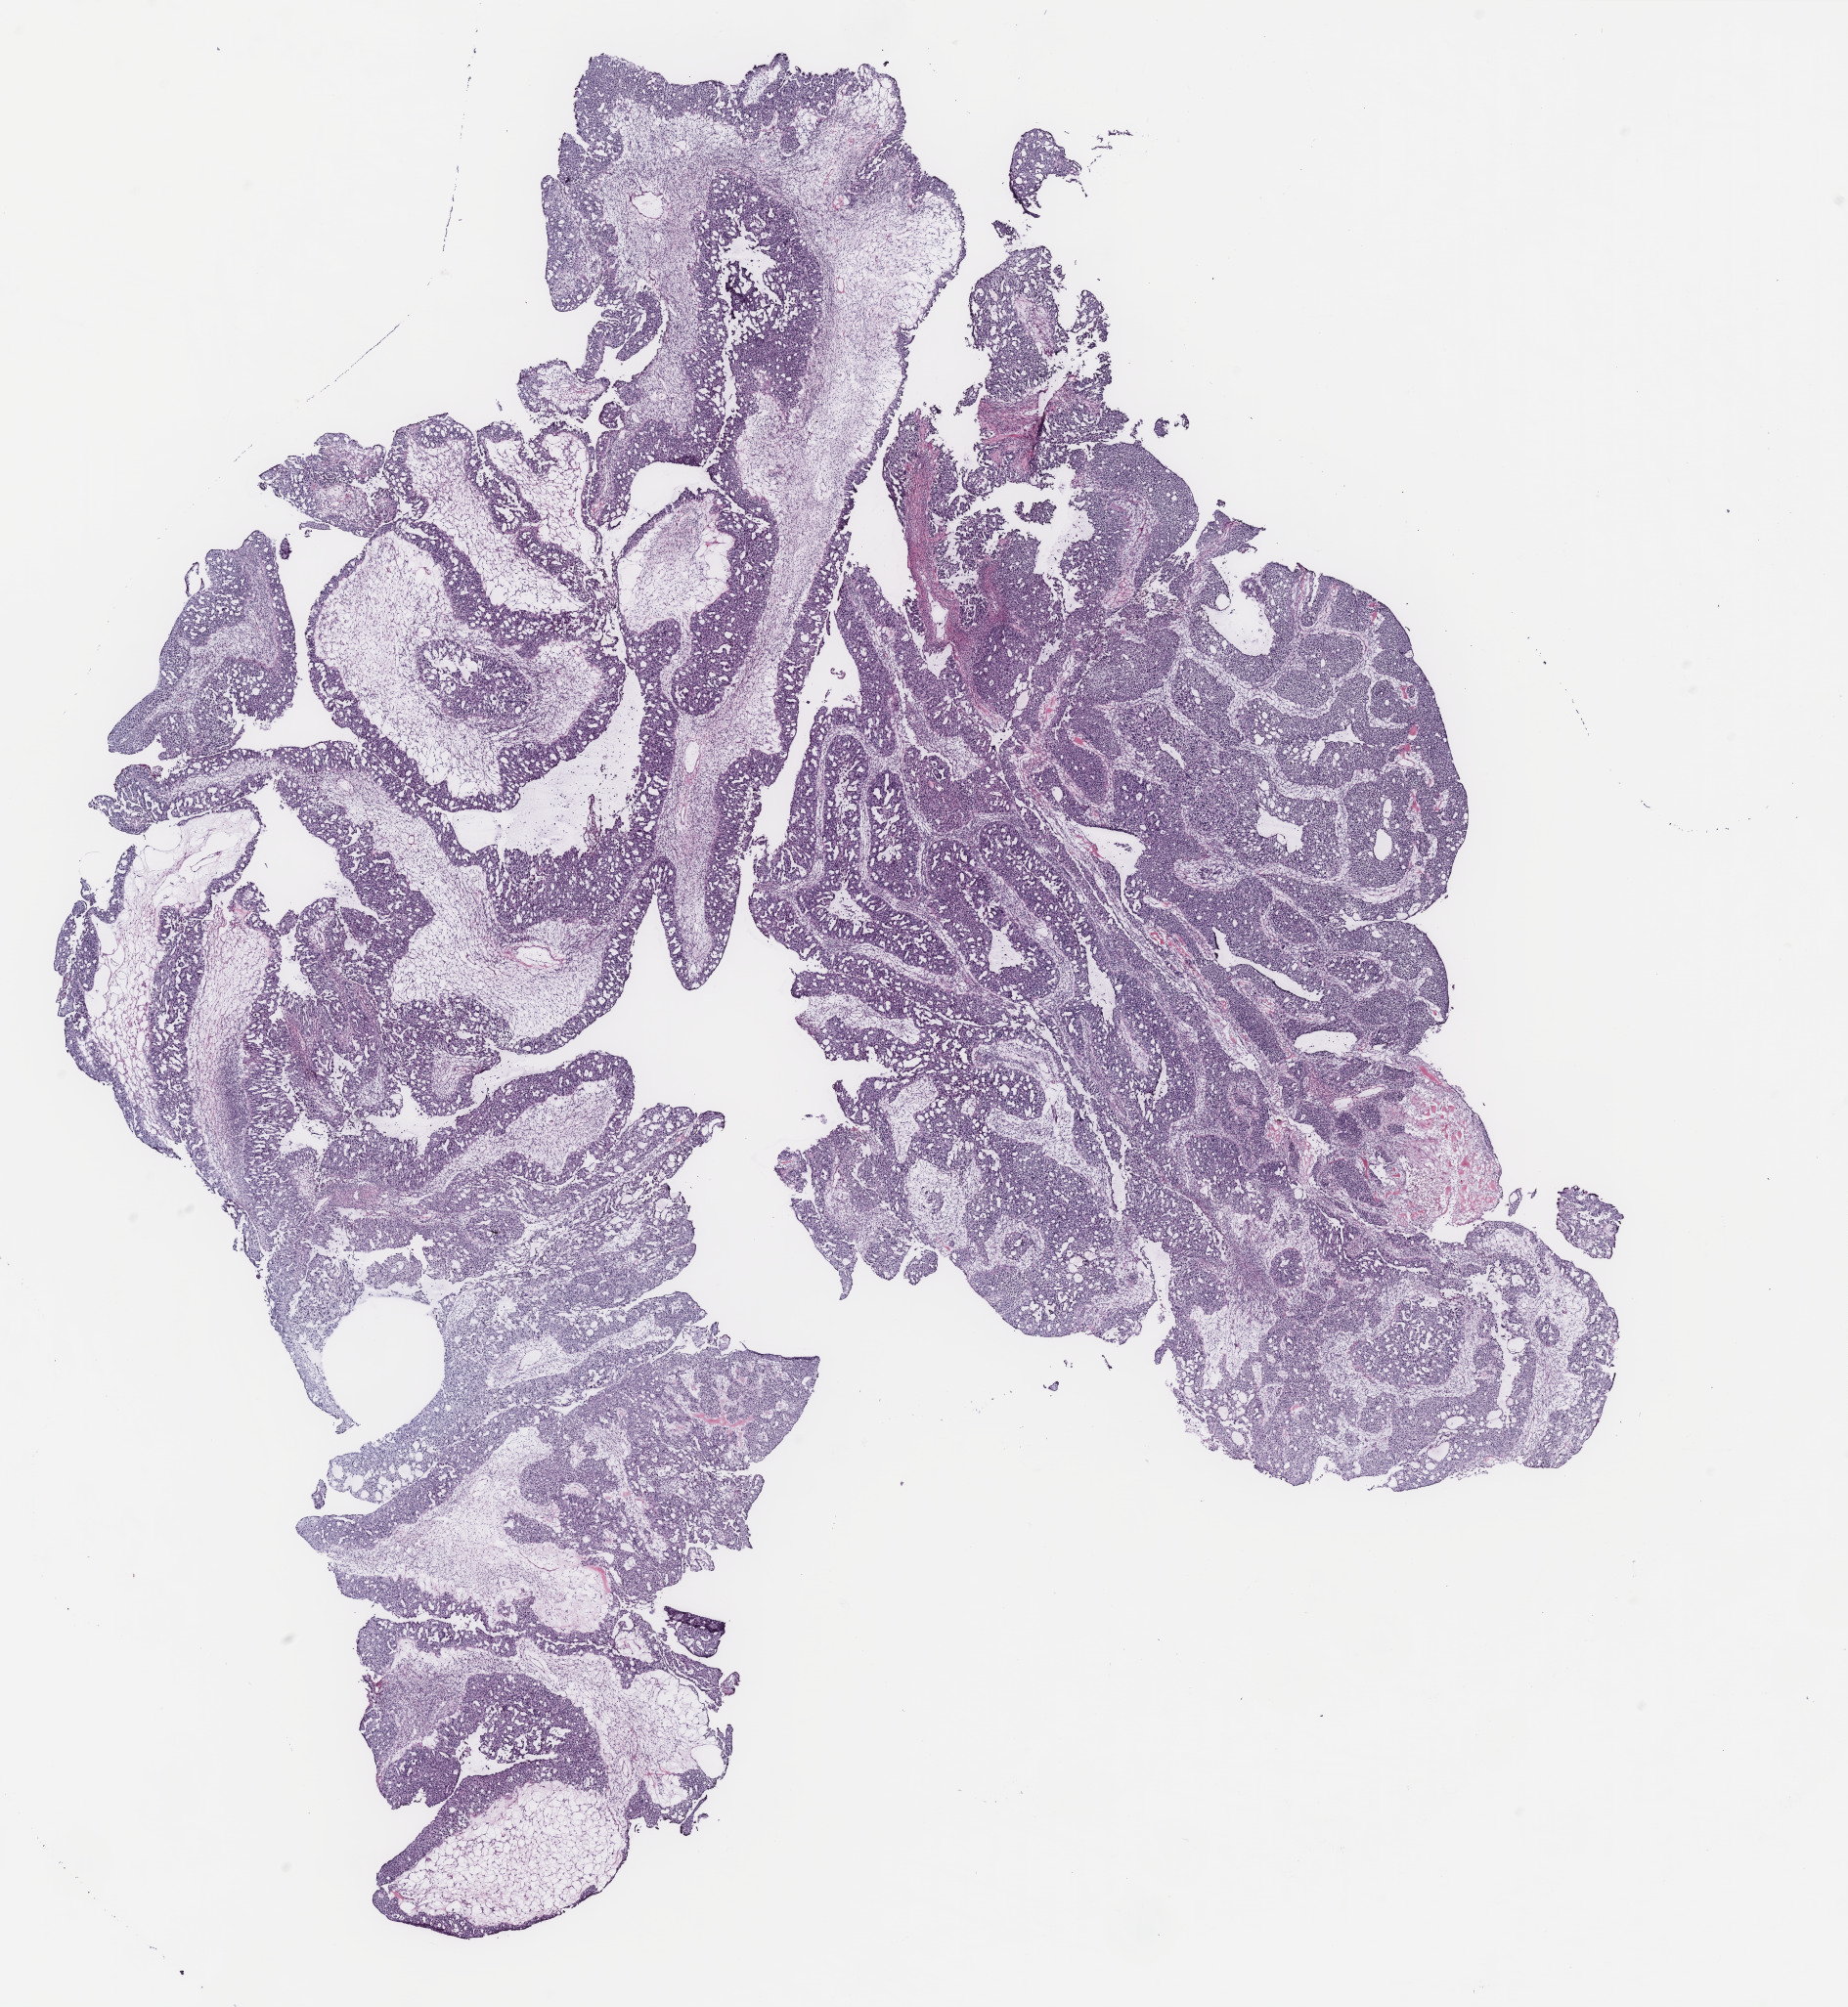
Whole-slide histology image, H&E-stained, shown as a low-resolution overview of the whole scanned area (about 15.1 x 16.4 mm, slide scanned at 40x); ovary, tumour tissue. Female, 70 y/o.
Histologic diagnosis: Serous adenocarcinoma, NOS. Primary tumour site (as recorded): ovary.